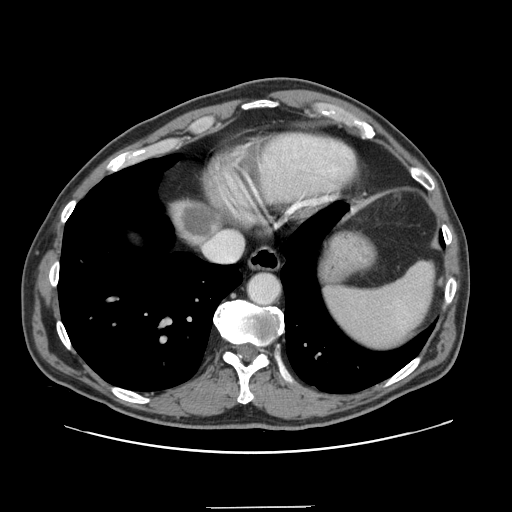
Contrast-enhanced abdominal CT, one axial slice. Position 131 of 139 along the scan axis. 120 kVp. Intravenous contrast given. Soft-tissue window (W 400 / L 40 HU). 512 × 512 image matrix, field of view 397 × 397 mm. Male patient, age 64 years. From the clinical record (not read from this slice): diagnosis: colorectal cancer liver metastases, imaged before liver resection; multiple liver metastases: yes; largest metastasis: 3.5 cm; disease in both lobes: yes.
Structures marked on this image (outlined manually by an expert reader):
- liver: bounding box (x1, y1, x2, y2) in pixels: (173, 202, 219, 245)
- liver metastasis: (183, 206, 218, 238)